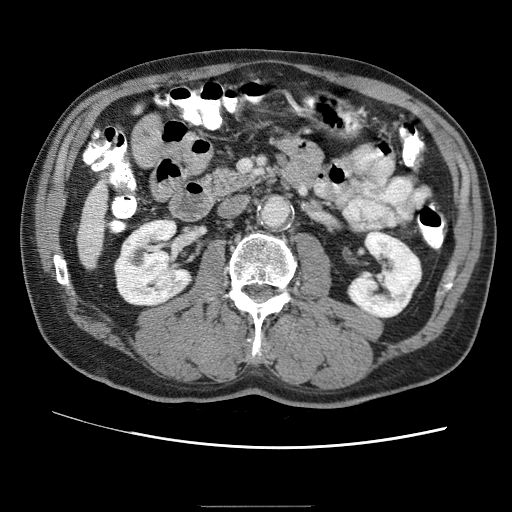
Contrast-enhanced abdominal CT (liver protocol), one axial slice. Slice 5 of 75 in the series (ordered by position). 120 kVp. One of 2 acquisitions stored at this slice position. Soft-tissue window (W 400 / L 40 HU). 2.5 mm slice thickness. 512 × 512 image matrix, field of view 360 × 360 mm. Case-level facts recorded for this patient, not image findings: diagnosis: hepatocellular carcinoma (patient treated with transarterial chemoembolisation; whether this scan precedes or follows treatment is not stated here); TNM stage (as recorded): Stage-II; Child-Pugh class: A; tumour size: 2 cm.
Annotated regions visible in this slice (semi-automatic segmentation, software-assisted and operator-edited):
- liver parenchyma outside the tumour (the mass and vessels are separate outlines, so this box may not span the whole liver): box from (x=80, y=194) to (x=98, y=252) px
- liver vessels: (x=82, y=198)–(x=96, y=246)